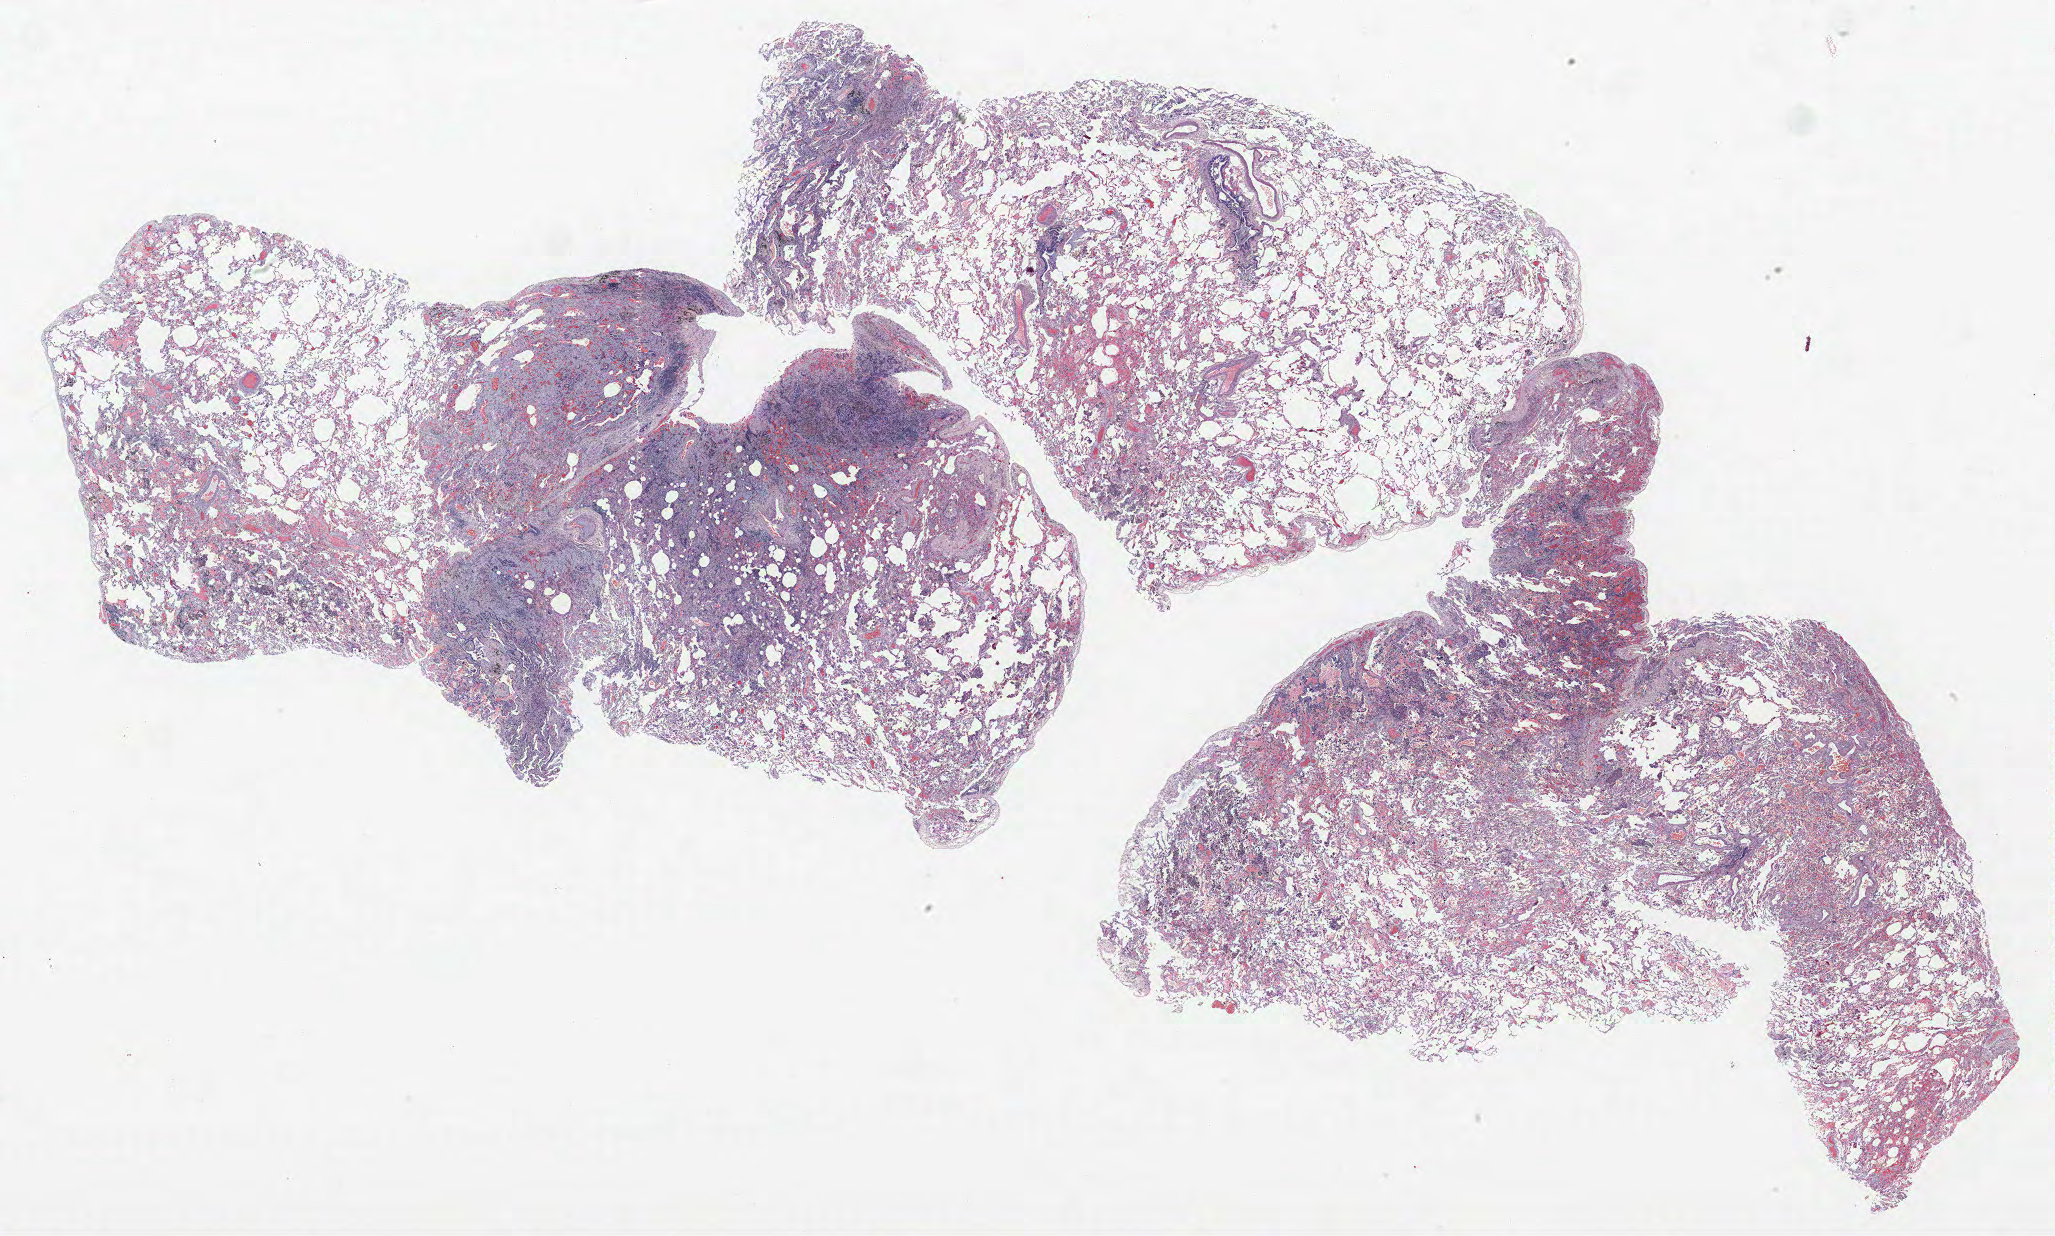
Whole-slide histology image, Hematoxylin and eosin (H&E) stained — low-resolution overview of the scanned area, about 32.9 x 19.8 mm, formalin-fixed paraffin-embedded (FFPE) section, lung tissue. Male, age 56 at enrolment. Former smoker at enrolment.
Participant's lung-cancer diagnosis: Adenocarcinoma, NOS.